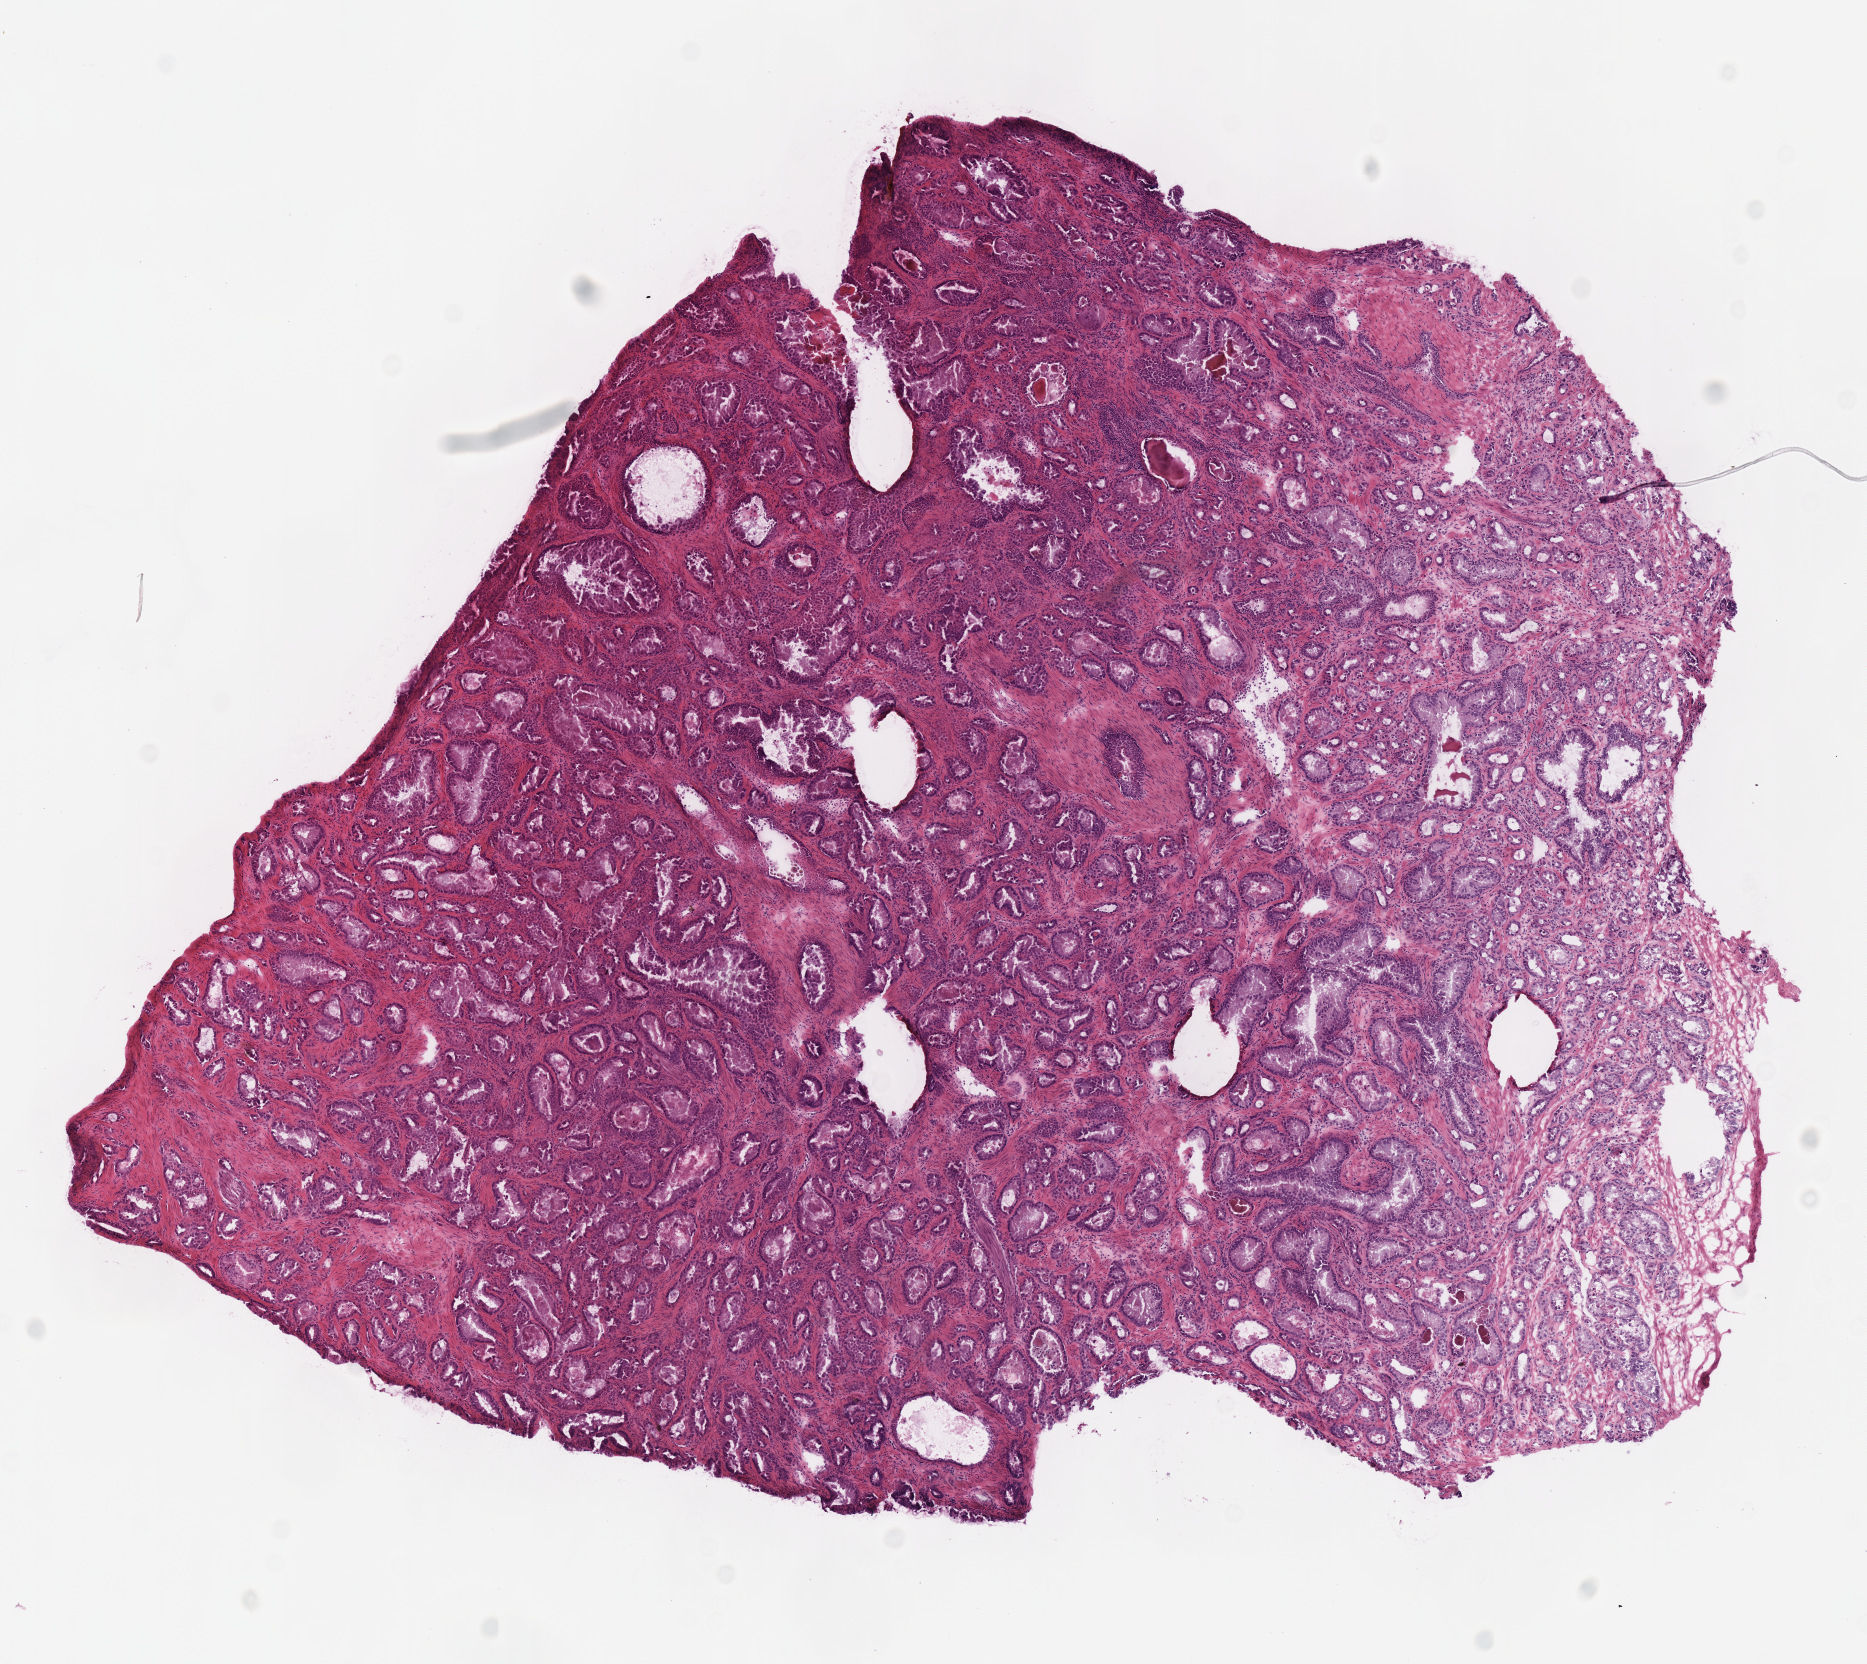
Hematoxylin and eosin (H&E) stained whole-slide image, a low-resolution overview of the entire scanned area, about 7.3 x 6.5 mm, frozen section from the top of the tissue portion, prostate, primary tumour sample. Male patient; age at initial diagnosis 59 years. Gleason score: 7 (3+4). Composition of this section per pathologist review: tumour nuclei 65%, necrosis 0%.
Diagnosis: Acinar cell carcinoma (prostate gland).